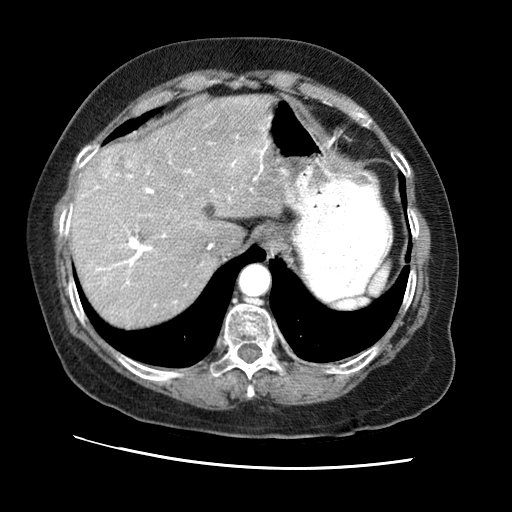
Contrast-enhanced abdominal CT (liver protocol), one axial slice. Position 51 of 65 along the scan axis. 120 kVp. Soft-tissue window (W 400 / L 40 HU). 2.5 mm slice thickness. 512 × 512 image matrix, field of view 340 × 340 mm. Case-level facts recorded for this patient, not image findings: diagnosis: hepatocellular carcinoma (patient treated with transarterial chemoembolisation; whether this scan precedes or follows treatment is not stated here); TNM stage (as recorded): Stage-II; Child-Pugh class: A; tumour differentiation: no biopsy; tumour nodularity: multinodular.
Annotated regions visible in this slice (semi-automatic segmentation, software-assisted and operator-edited):
- abdominal aorta: bounding box <240,265,269,295> (left, top, right, bottom; pixels)
- liver parenchyma outside the tumour (the mass and vessels are separate outlines, so this box may not span the whole liver): <68,94,289,326>
- mass: <96,143,139,185>
- liver vessels: <68,127,268,303>